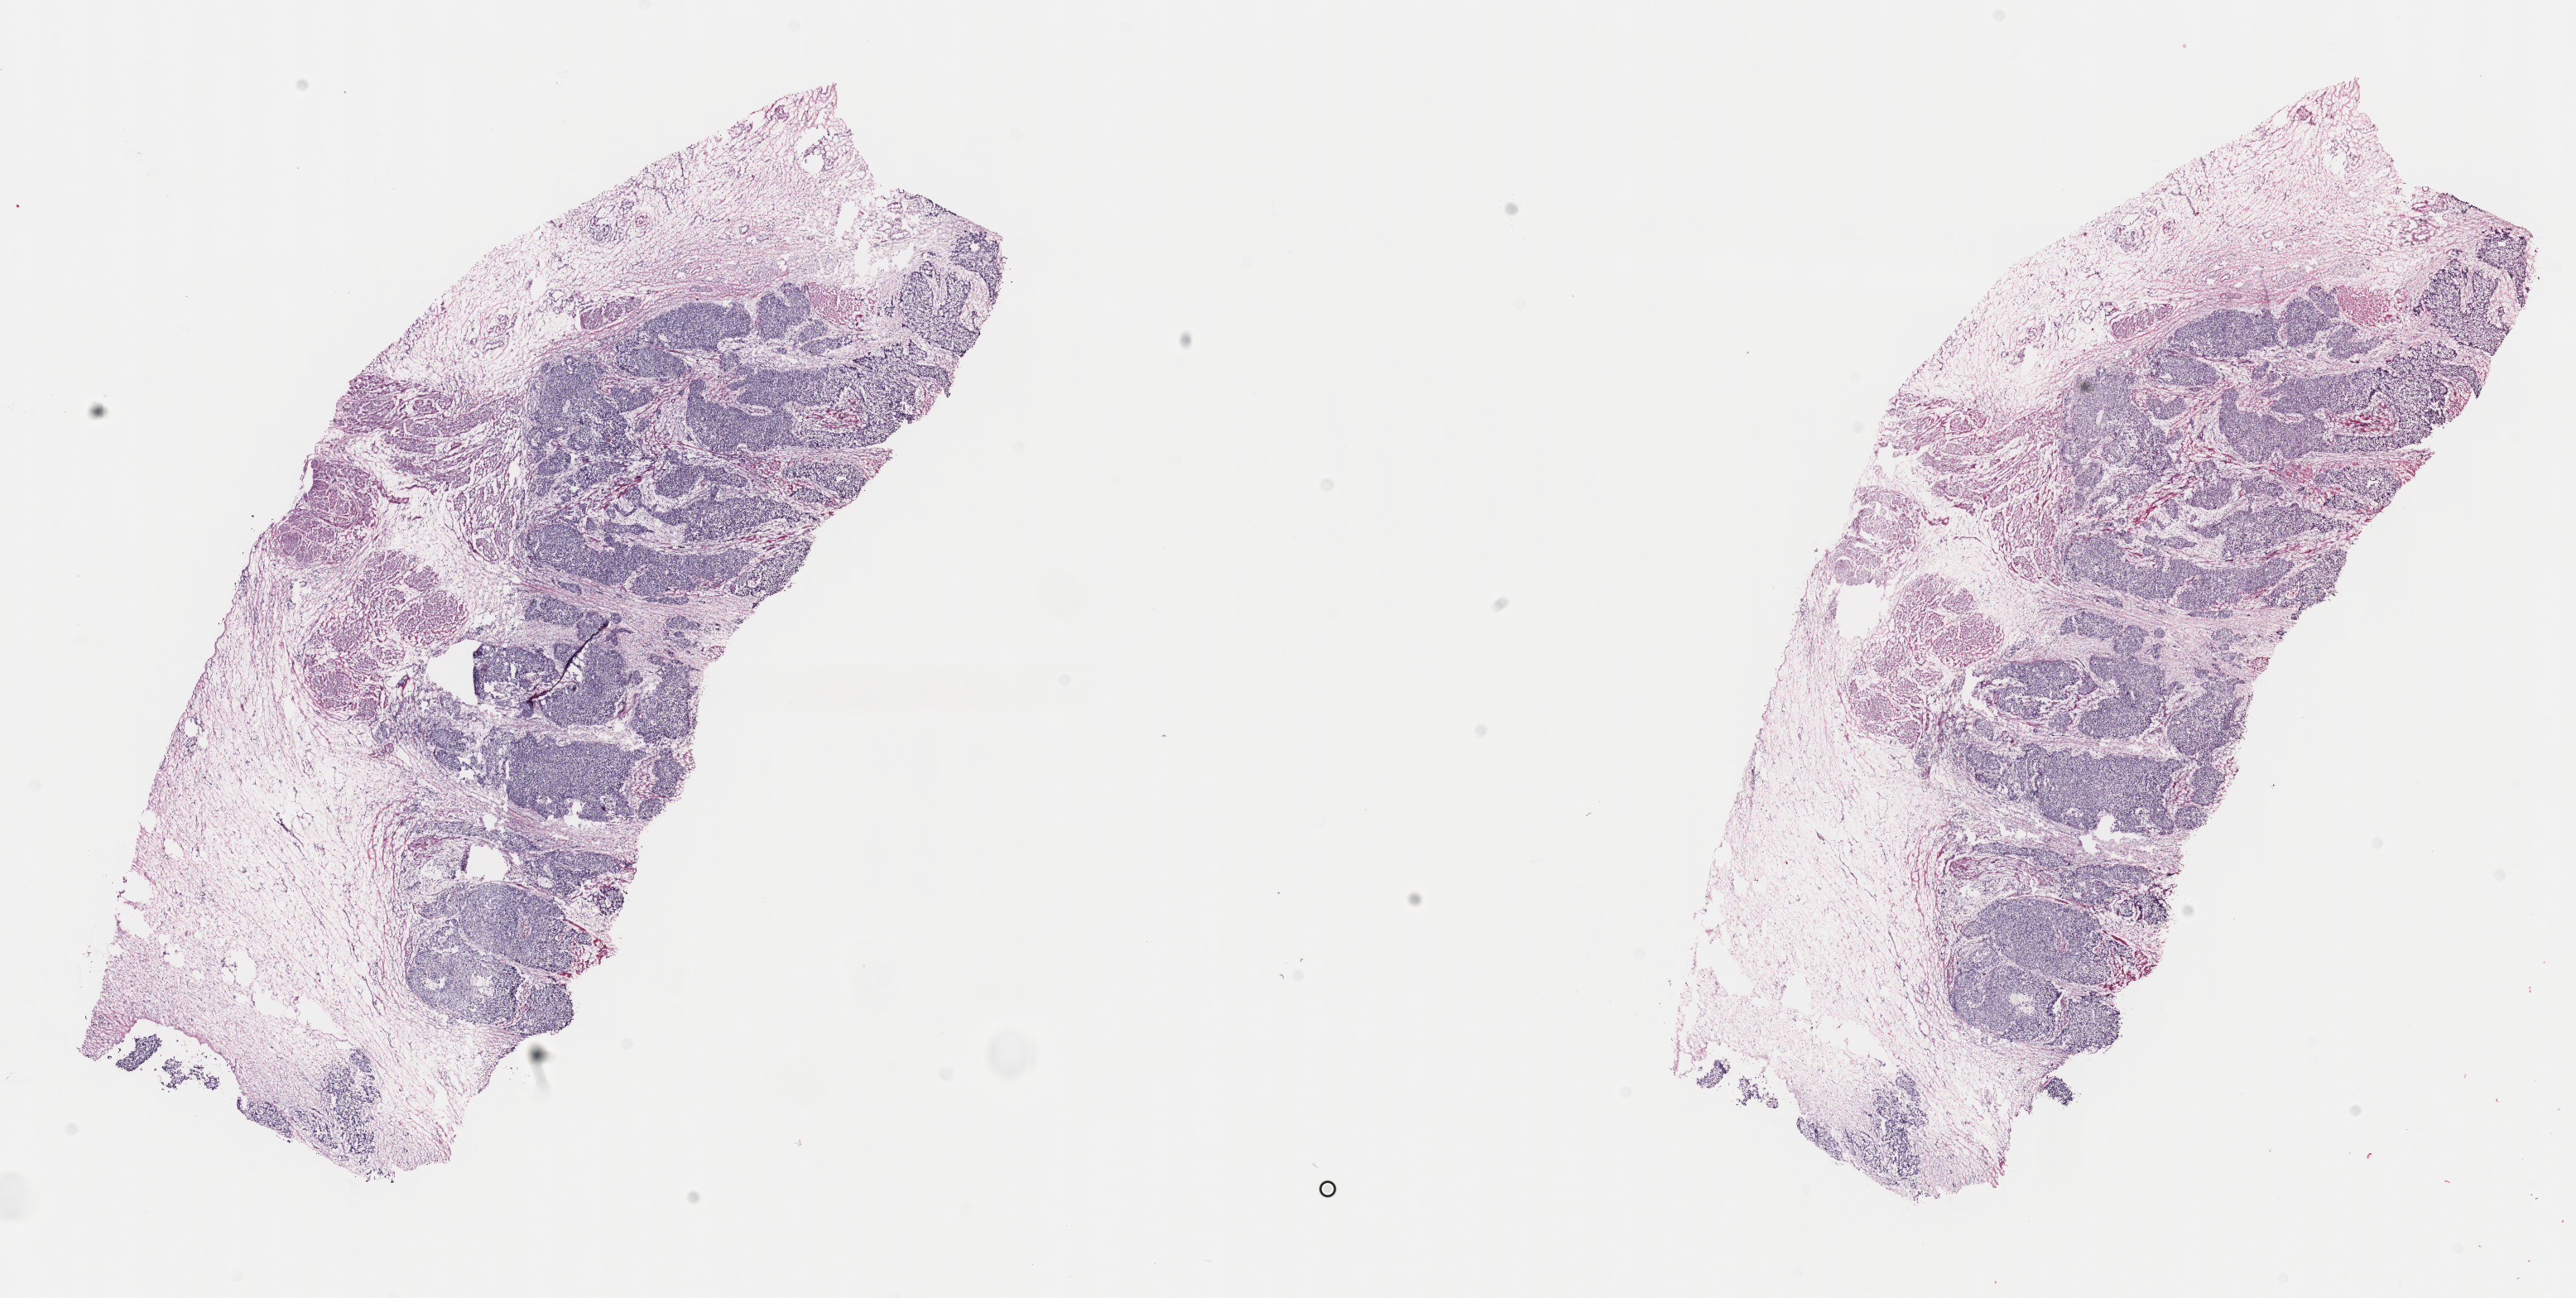
H&E-stained whole-slide image — low-resolution overview of the scanned area, about 25.2 x 12.7 mm (acquisition: 40x scan), frozen section, primary tumour sample from the bladder. Male, age 78 years at initial diagnosis. Histologic grade: high grade. Slide review estimates, as recorded: tumour cells 75%, tumour nuclei 75%, normal cells 0%, stromal cells 25%, necrosis 0%. Inflammatory infiltration, as recorded: lymphocyte infiltration 4%, monocyte infiltration 1%, neutrophil infiltration 3%.
Diagnosis: Papillary transitional cell carcinoma. TNM: T3b N0 MX. AJCC pathologic stage: III (5th edition). Lymph nodes positive (case pathology): 0 of 13 examined.